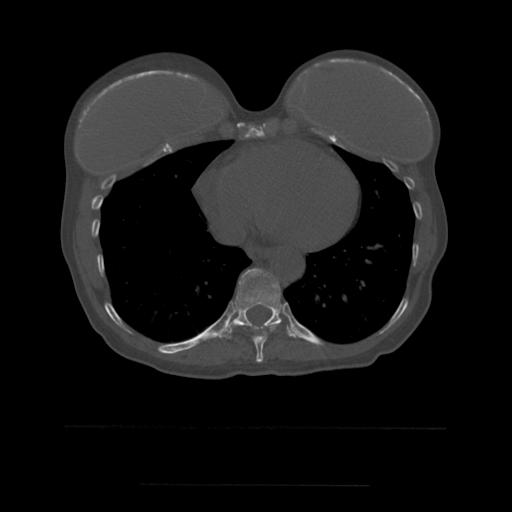
CT including the spine, one axial slice. Slice 310 of 544 in the series (ordered by position). Bone window (W 1800 / L 400 HU). 1.25 mm slice thickness. 512 × 512 image matrix. Patient age 58 years. From the clinical record (not read from this slice): primary cancer: lung.
Annotated regions visible in this slice (semi-automatic segmentation, software-assisted and operator-edited):
- T10 vertebra: box from (x=217, y=269) to (x=296, y=339) px
- T9 vertebra: (x=244, y=323)–(x=280, y=363)